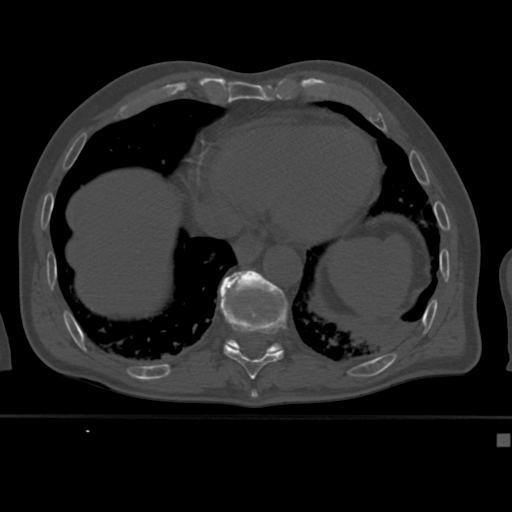
CT including the spine, one axial slice; reconstruction kernel Br40s; bone window (W 1800 / L 400 HU); 1.5 mm slice thickness; 512 × 512 image matrix, field of view 337 × 337 mm. Male patient, age 64 years. Case-level facts recorded for this patient, not image findings: primary cancer: uterus; vertebrae with lytic lesions (as recorded): T1, T4, T5, T7, L5.
Structures marked on this image (semi-automatic segmentation, software-assisted and operator-edited):
- T10 vertebra: bounding box (x1, y1, x2, y2) in pixels: (220, 300, 288, 380)
- T11 vertebra: (219, 270, 286, 354)